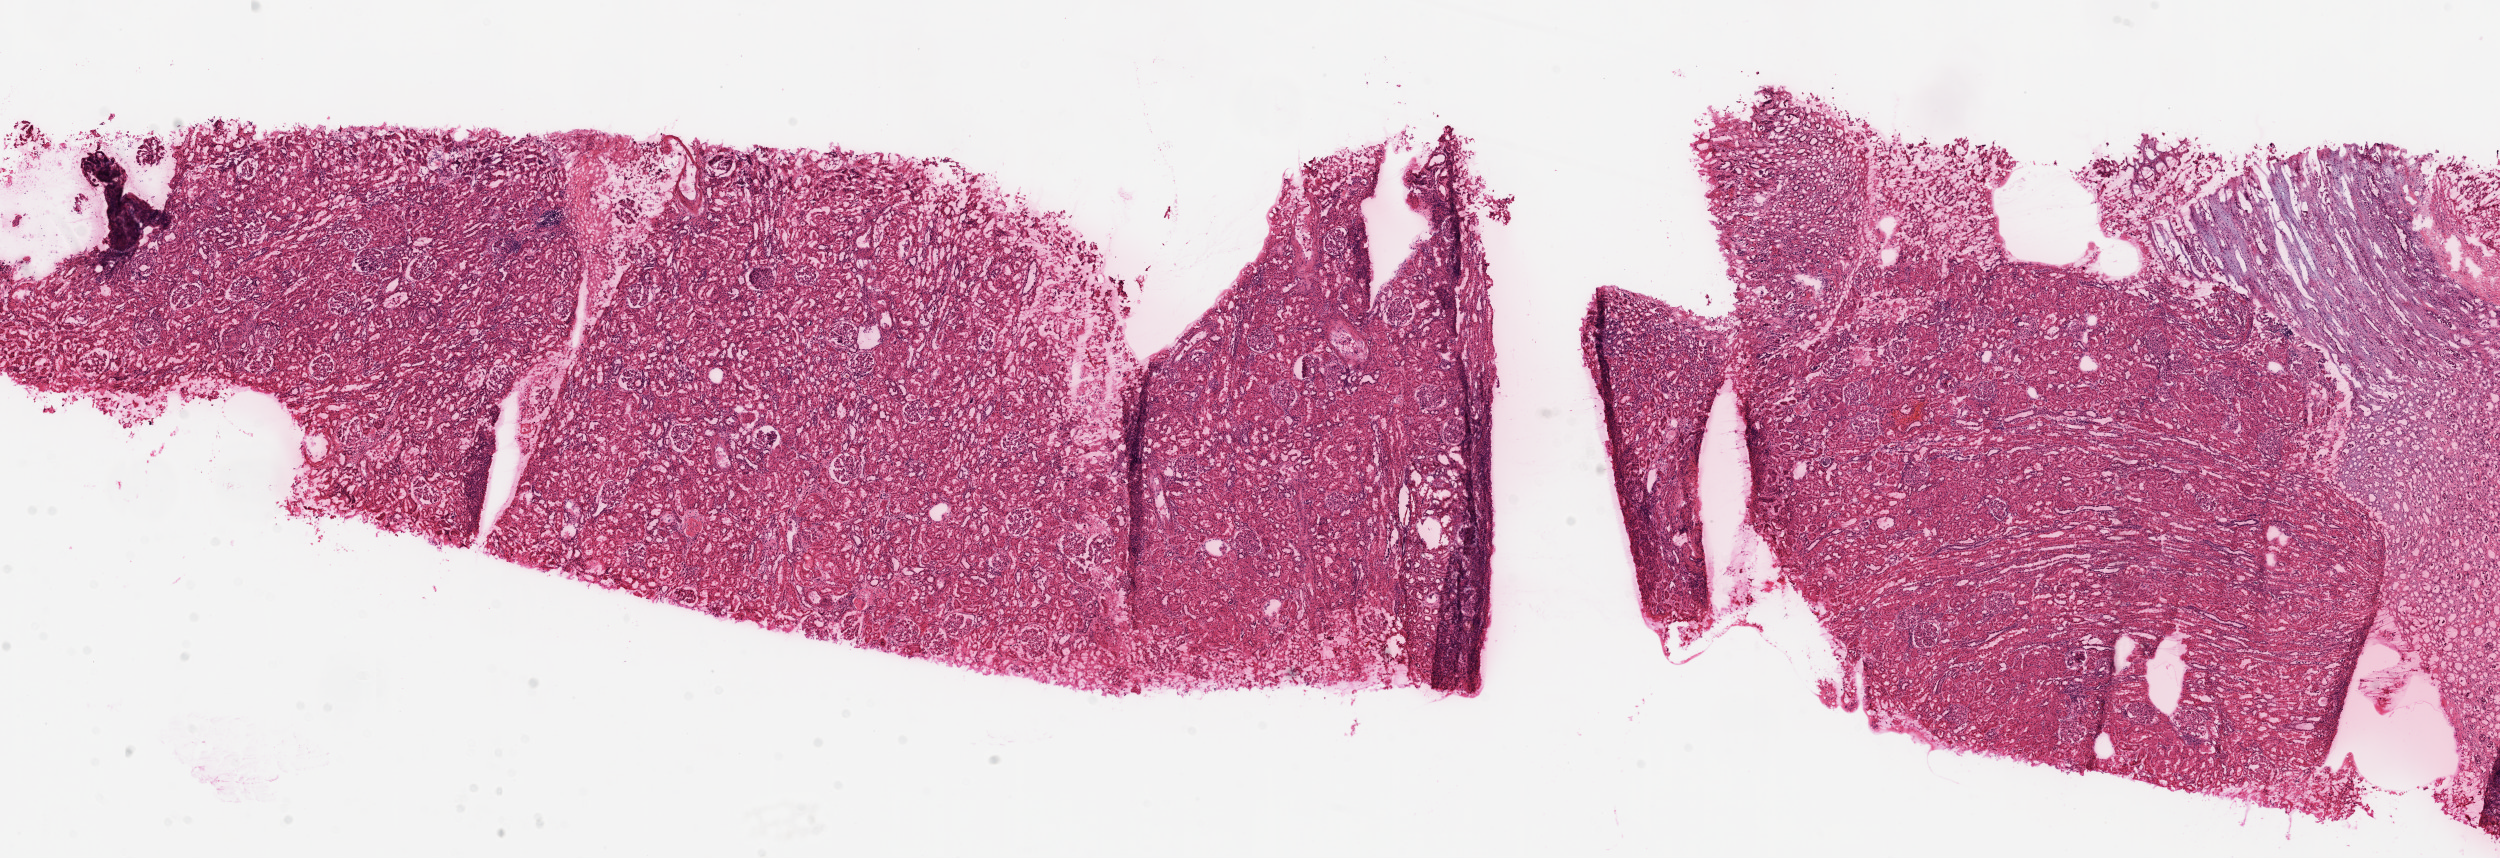
H&E whole-slide image — shown as a low-resolution overview of the whole scanned area (about 20.1 x 6.9 mm). Frozen section. Kidney, solid tissue normal (non-tumour tissue) sample. Patient: female, age at initial diagnosis 63 years.
This section: solid tissue normal sample (biorepository sample class). Patient diagnosis: Clear cell adenocarcinoma, NOS.